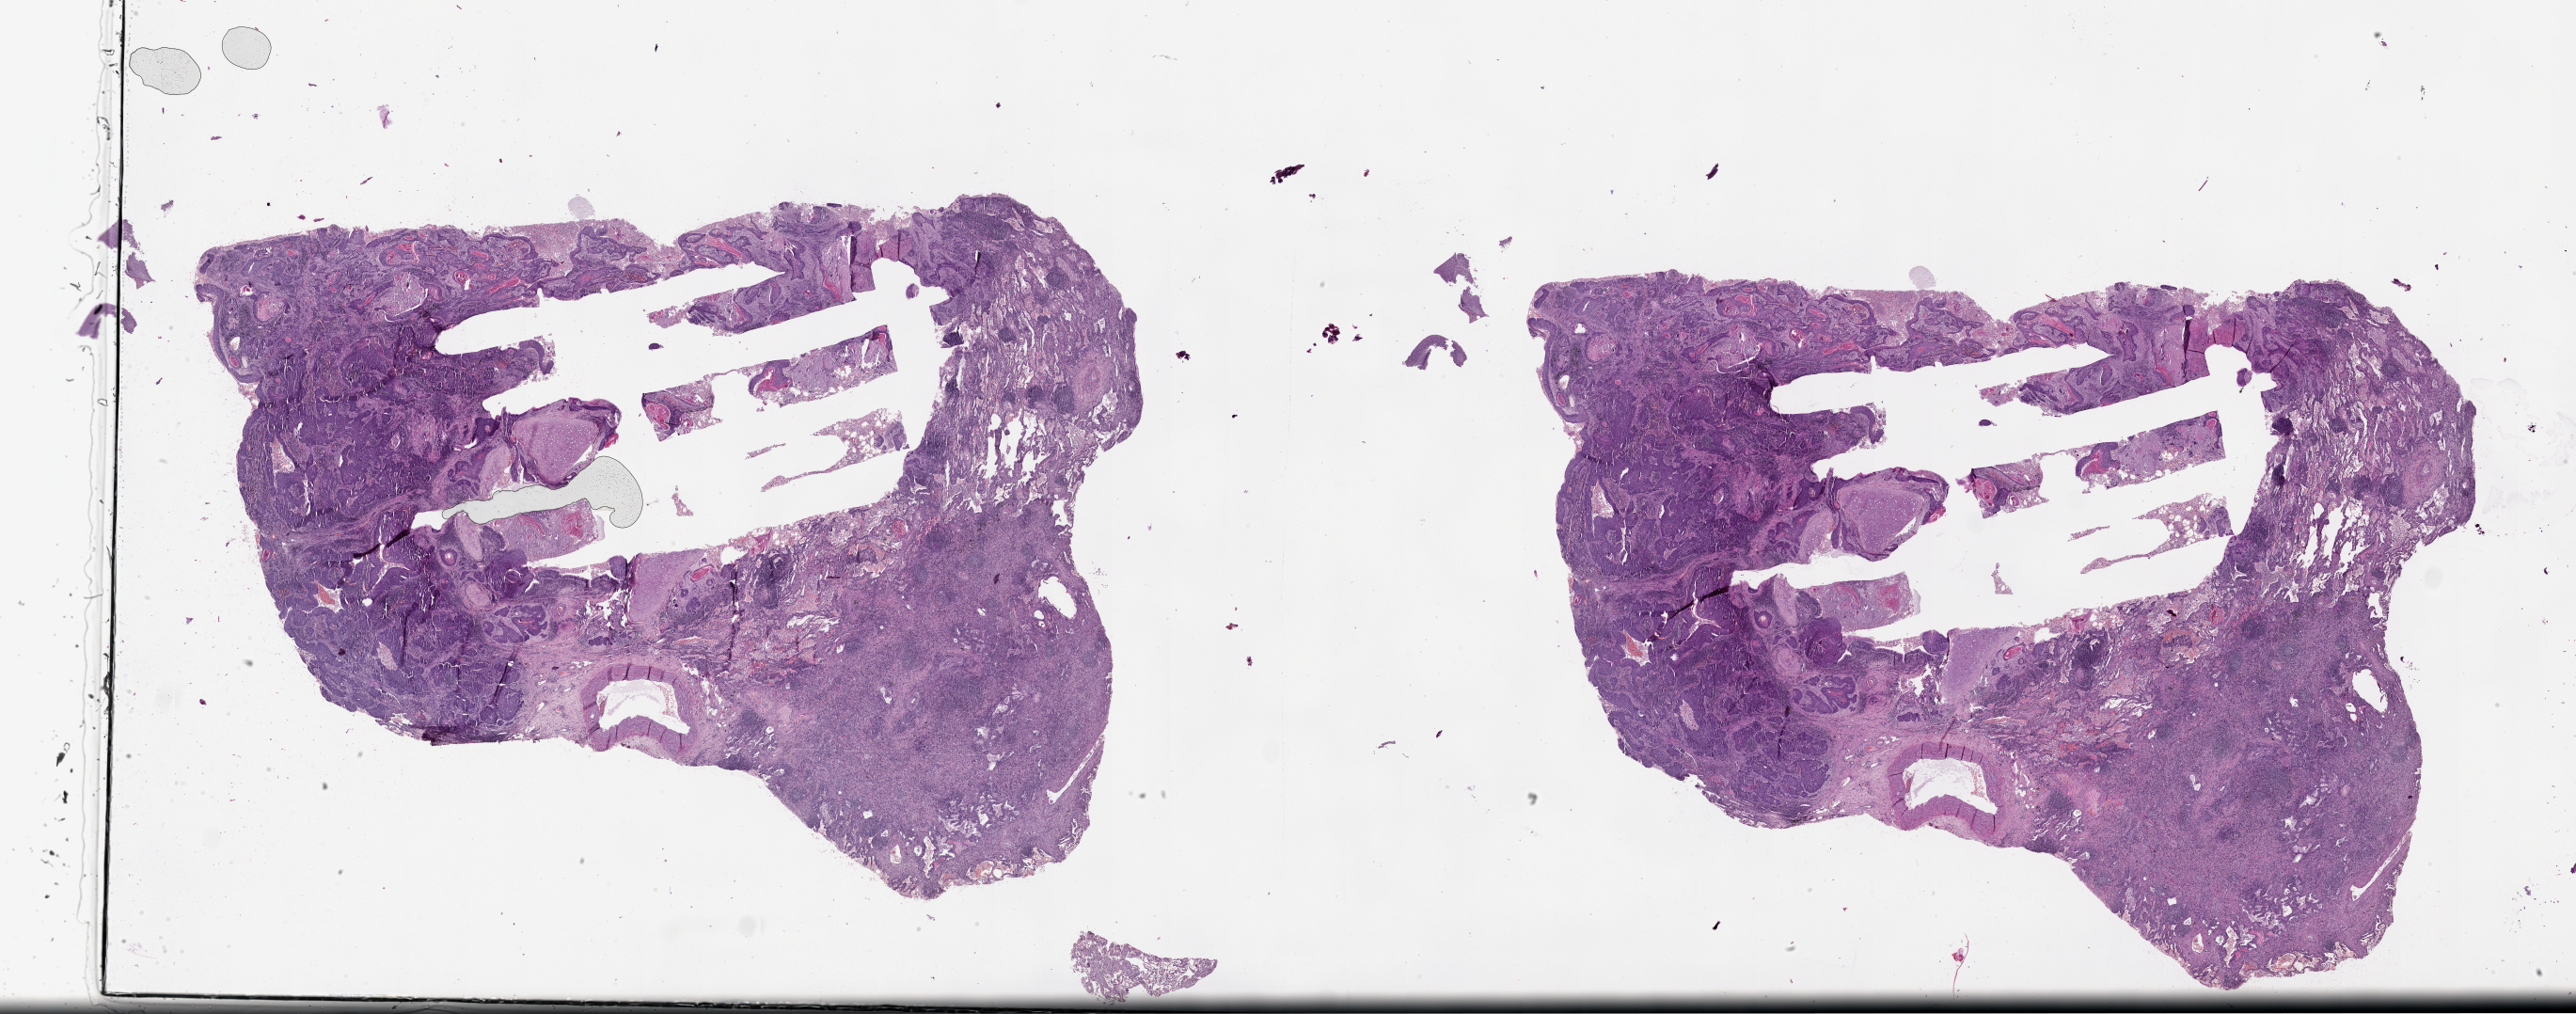
Whole-slide histology image, H&E — shown as a low-resolution overview of the whole scanned area (about 44.1 x 17.4 mm, from a 20x scan); tumour tissue sample, lung. Patient: male, age 72 years.
Patient diagnosis (cohort enrolment): squamous cell carcinoma (lung).